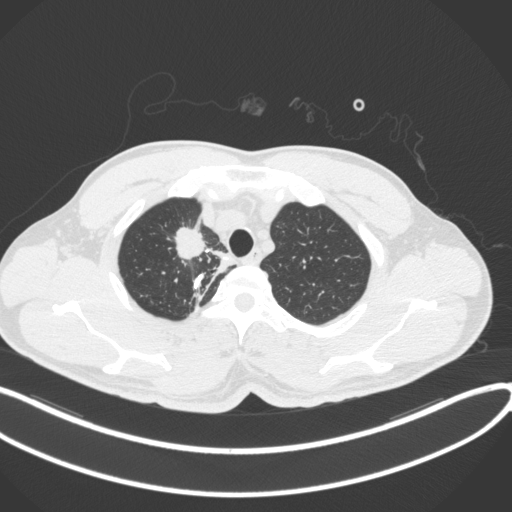
Chest CT, one axial slice. Reconstruction kernel B31f. 120 kVp. Lung window (W 1500 / L -600 HU). 1 mm slice thickness. 512 × 512 image matrix, field of view 400 × 400 mm. Male patient, age 48 years. Case-level facts recorded for this patient, not image findings: clinical TNM (as recorded): T1c N1 M1.
Structures marked on this image (bounding box drawn by a radiologist):
- lung tumour (recorded histology: adenocarcinoma): bounding box <170,223,208,265> (left, top, right, bottom; pixels)